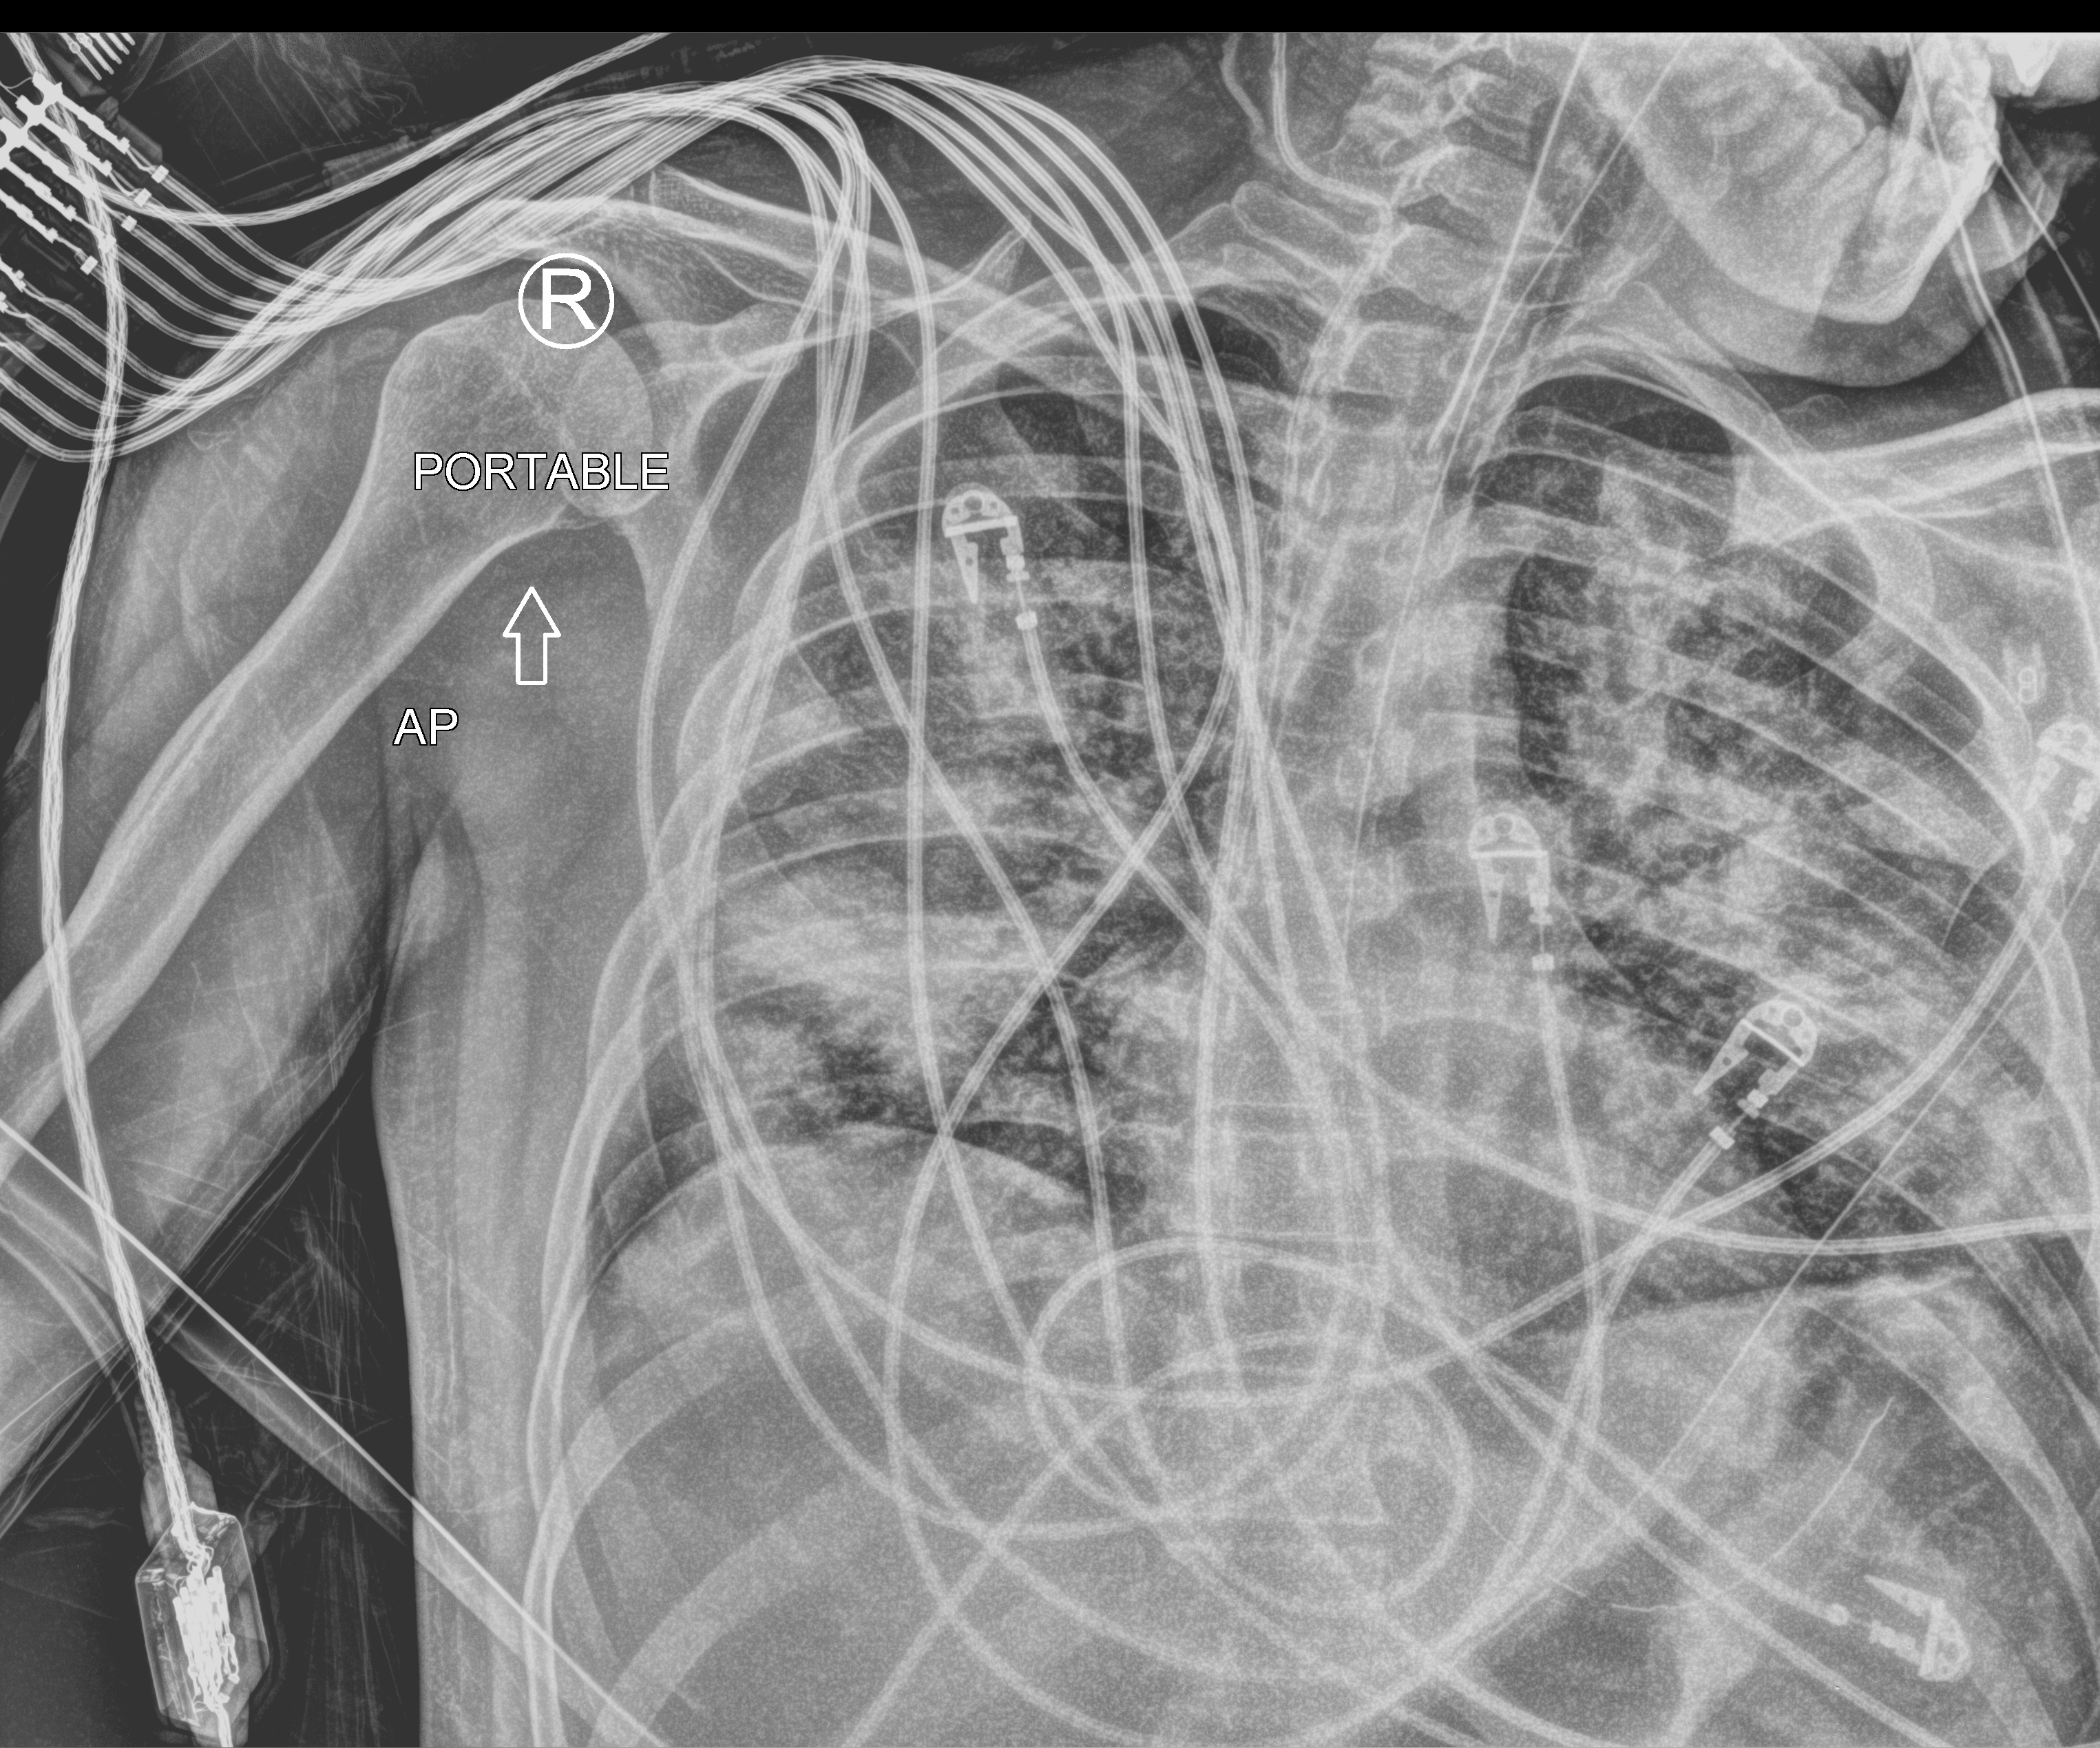
Chest X-ray (portable). Male patient hospitalised with COVID-19, age 18–59 years.
Admission-level facts for this patient (not findings on this image; timing relative to this image not recorded): mechanically ventilated during this hospital stay: yes; COPD (admission record): no; chronic kidney disease (admission record): no.